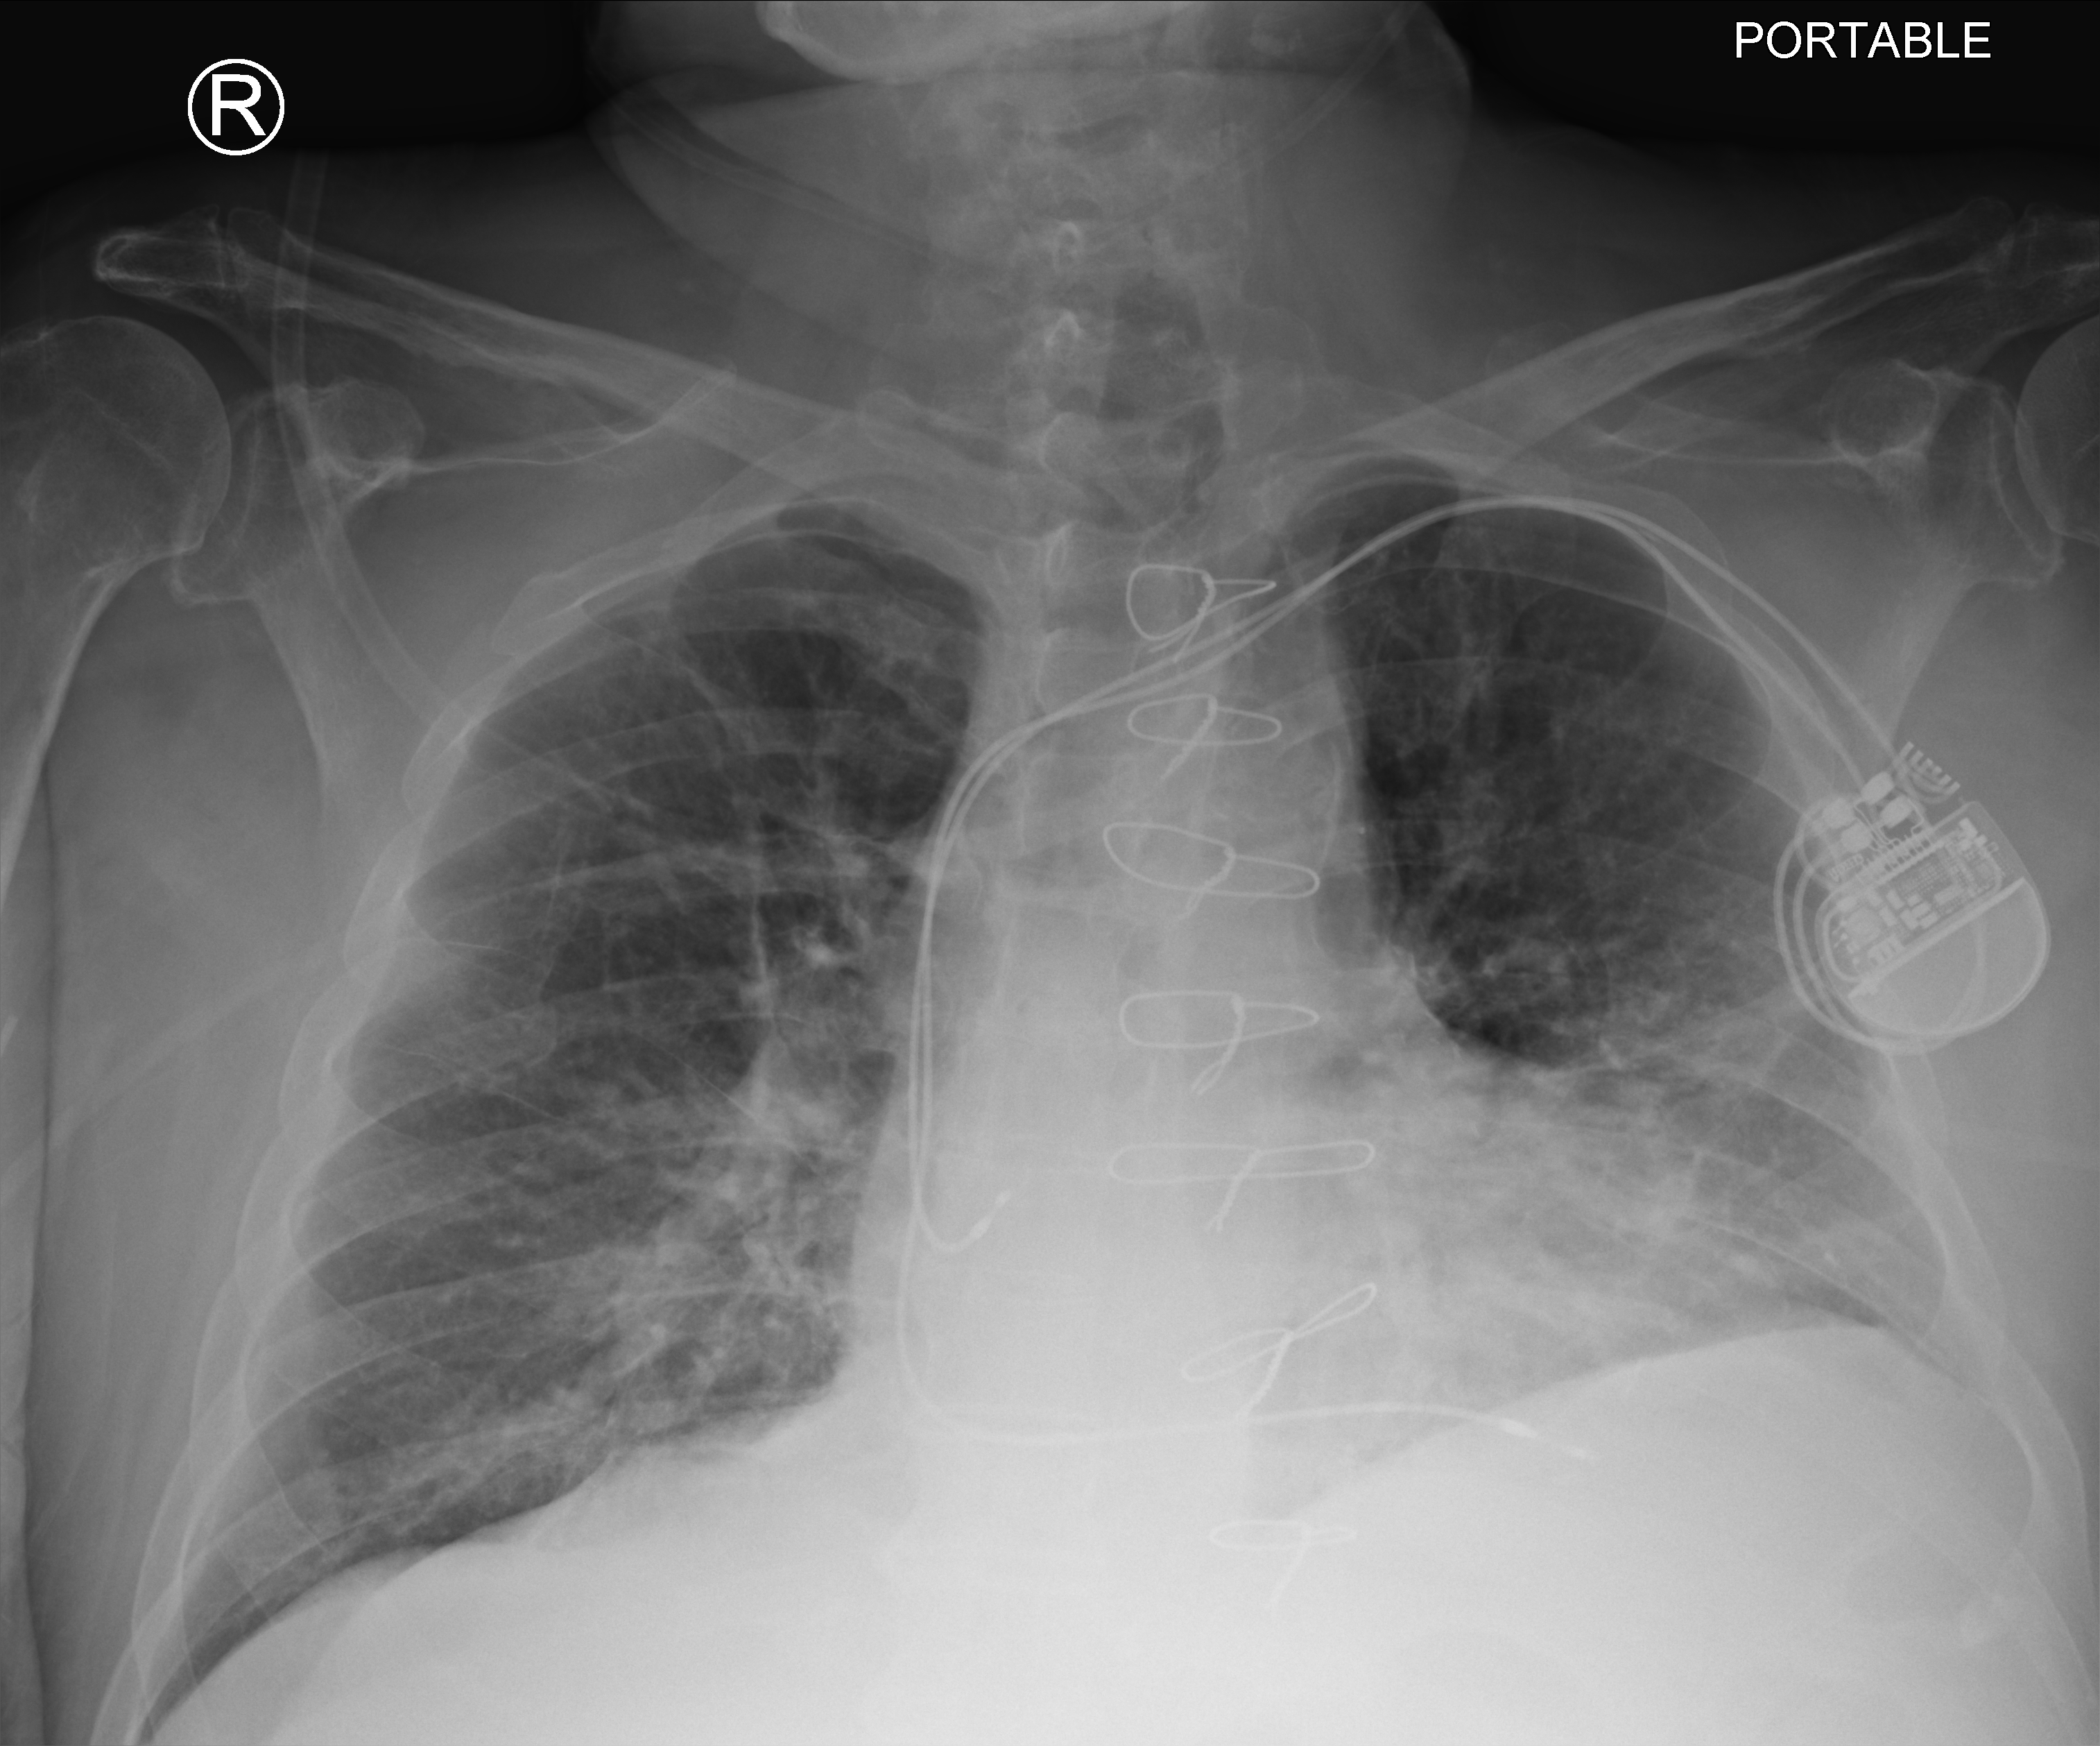
Bedside chest radiograph (computed radiography), anteroposterior (AP) projection. Male patient hospitalised with COVID-19, age 75–90 years.
From the hospital-stay record, not from the radiograph (when in the stay this image was taken is not recorded): mechanically ventilated during this hospital stay: no.